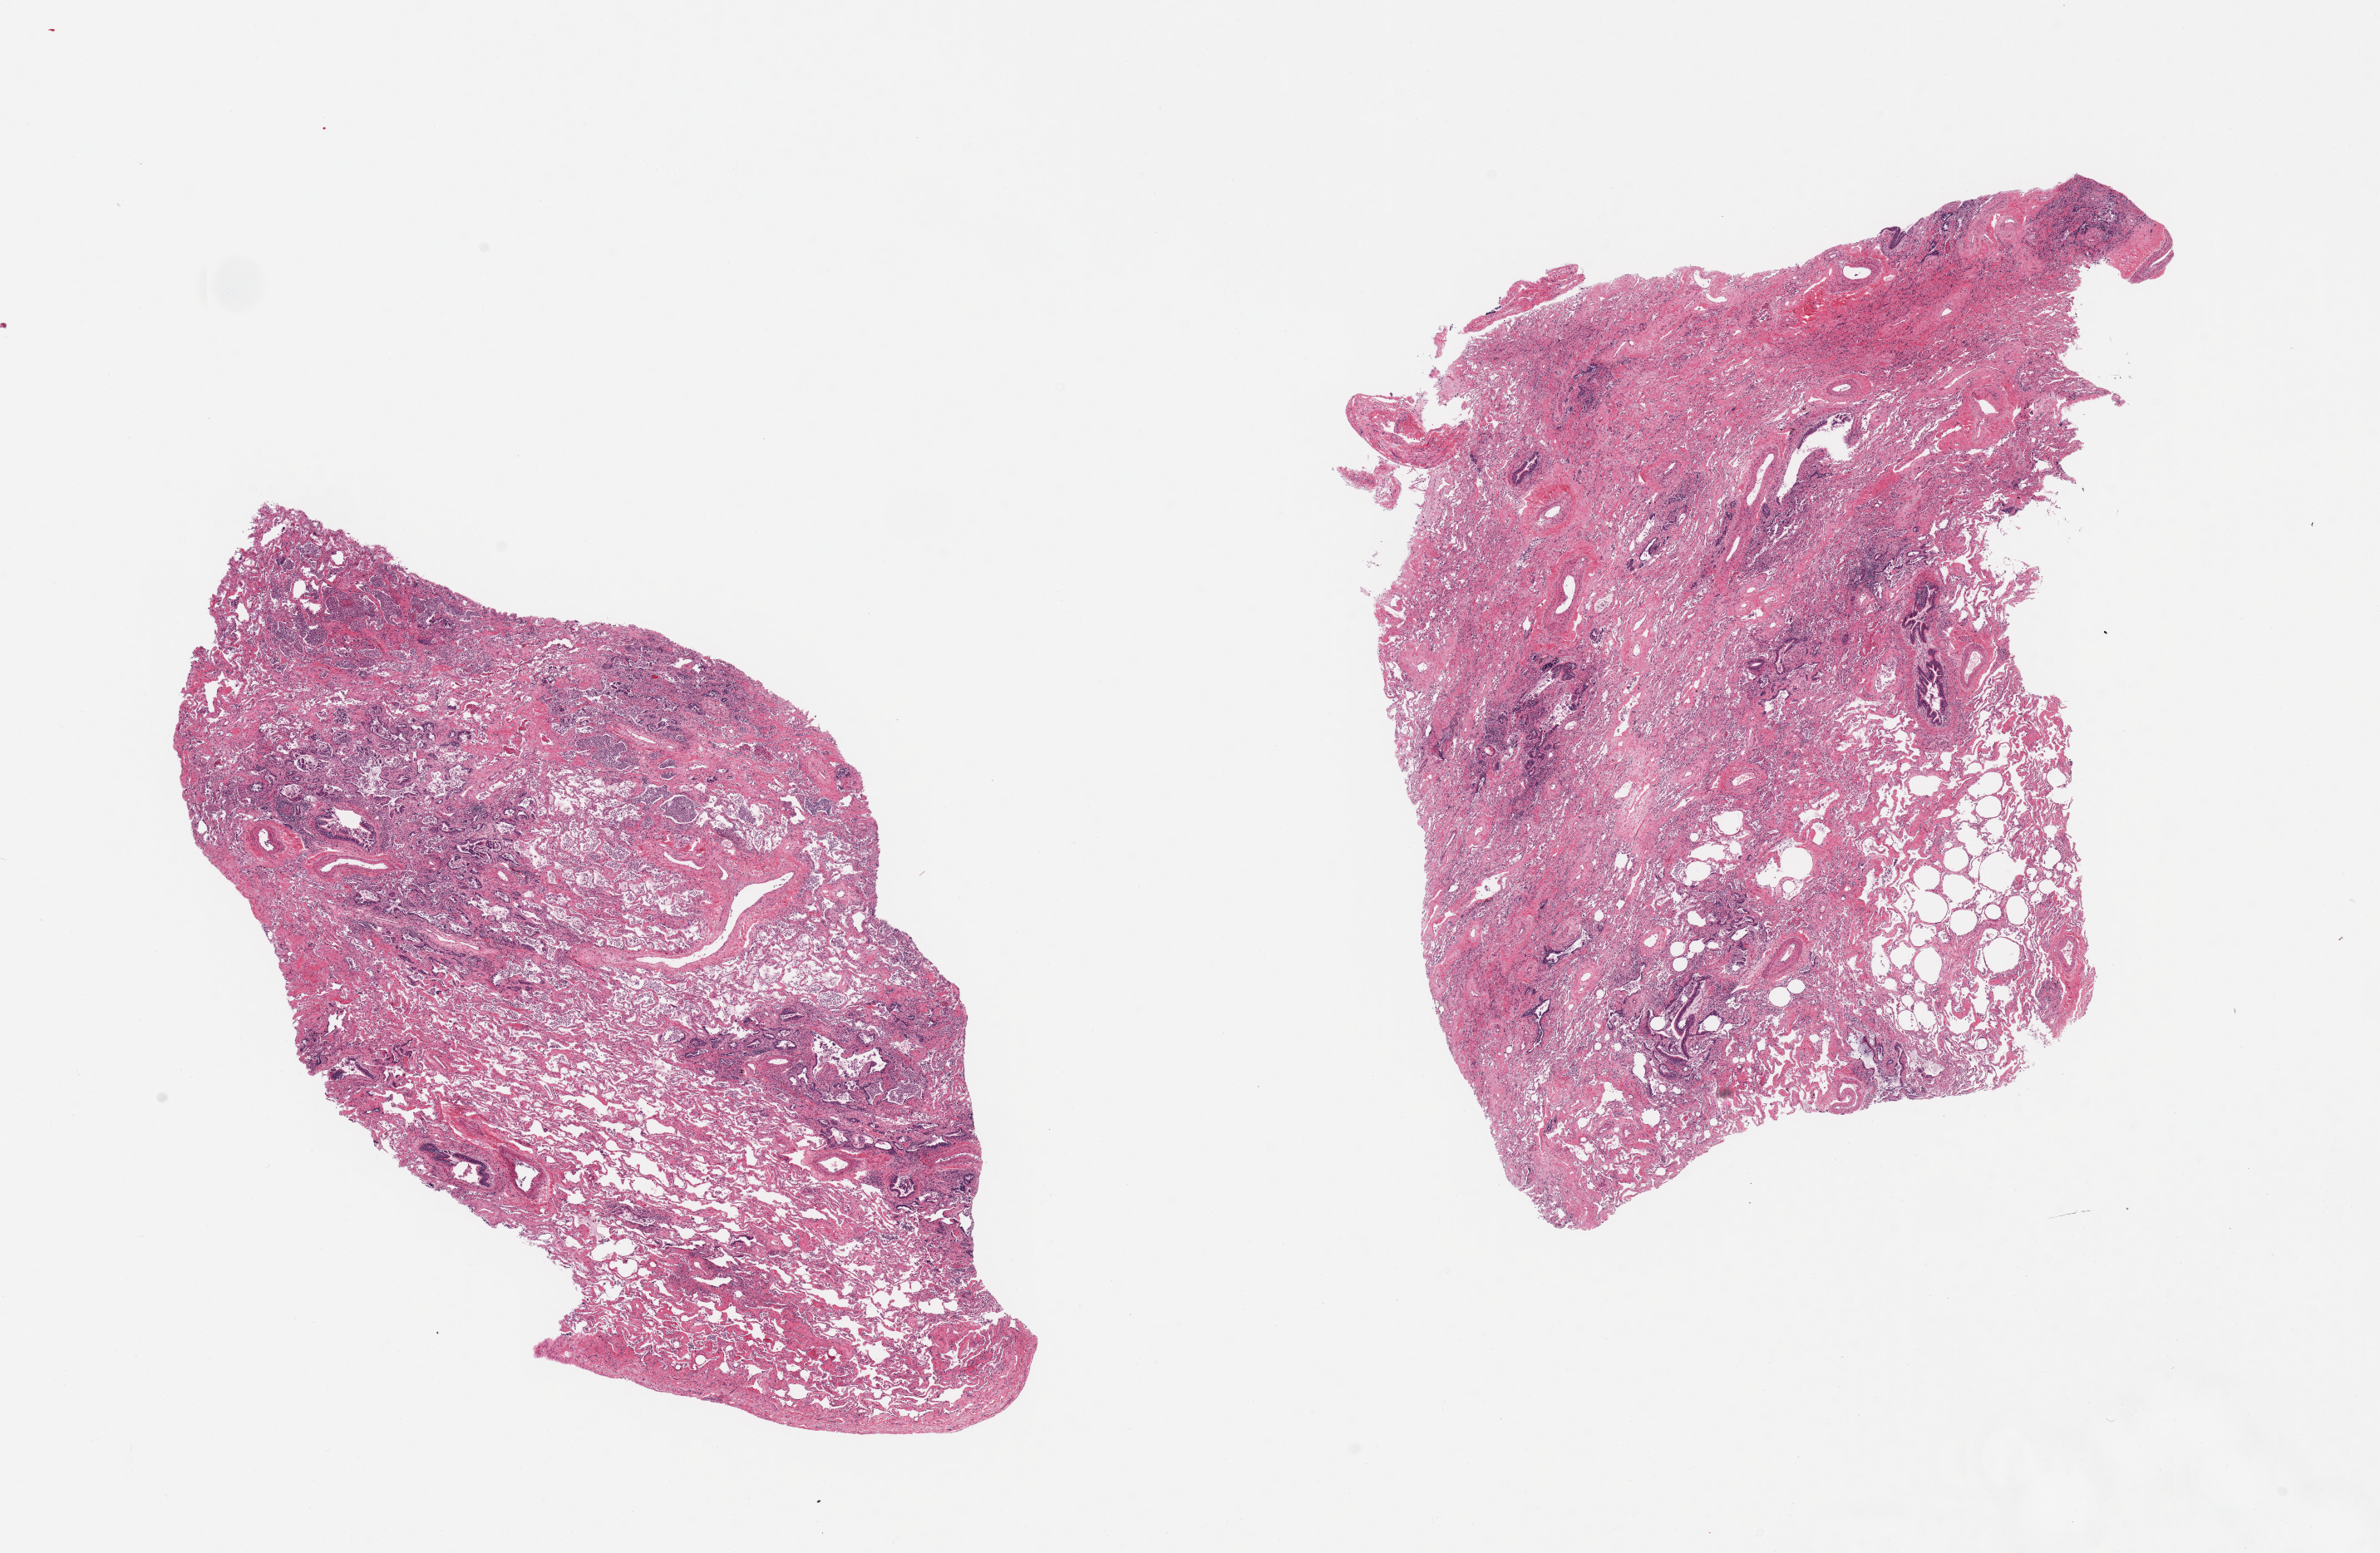
Hematoxylin and eosin (H&E) whole-slide image, shown as a low-resolution overview of the whole scanned area (about 22.6 x 14.8 mm). PAXgene-fixed, paraffin-embedded tissue. Target tissue: lung. Tissue donor sample.
Review note (as recorded): 2 pieces; extensive interstitial fibrosis; several foci of bronchopneumonia; <30% is relatively undamaged lung.